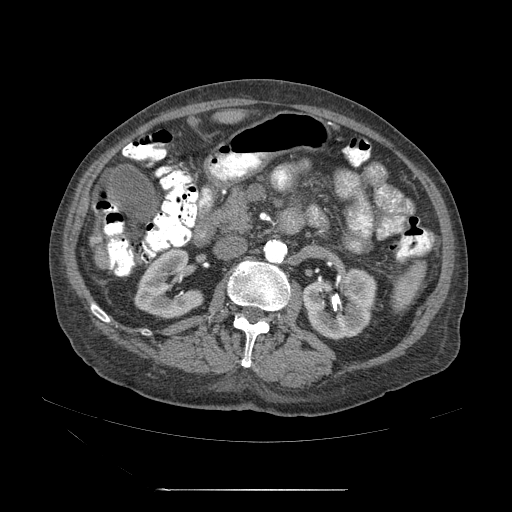
Contrast-enhanced abdominal CT (liver protocol), one axial slice; position 9 of 71 along the scan axis; reconstruction kernel STANDARD; 120 kVp; soft-tissue window (W 400 / L 40 HU); 2.5 mm slice thickness; 512 × 512 image matrix, field of view 440 × 440 mm. From the clinical record (not read from this slice): diagnosis: hepatocellular carcinoma (patient treated with transarterial chemoembolisation; whether this scan precedes or follows treatment is not stated here); TNM stage (as recorded): Stage-II; Child-Pugh class: A; tumour size: 1 cm.
Outlined on this slice (semi-automatically segmented with operator editing):
- abdominal aorta: bounding box [x1, y1, x2, y2] px = [264, 239, 286, 264]